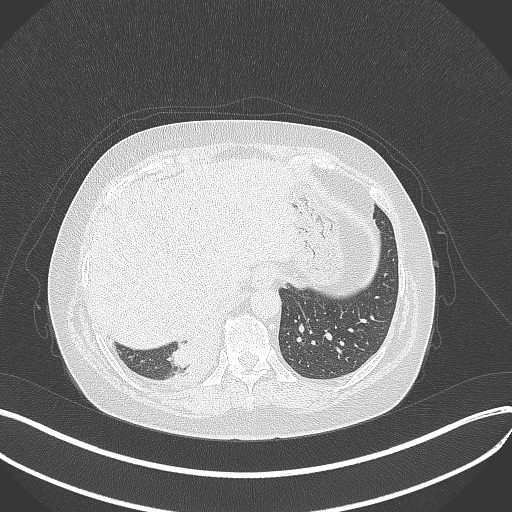
Chest CT, one axial slice; position 78 of 381 along the scan axis; reconstruction kernel B70f; 120 kVp; lung window (W 1500 / L -600 HU); 1 mm slice thickness; 512 × 512 image matrix, field of view 400 × 400 mm. Patient: female, 56 years. From the clinical record (not read from this slice): clinical TNM (as recorded): T2b N1 M0; histopathological grade: G3.
Annotated regions visible in this slice (bounding box drawn by a radiologist):
- lung tumour (recorded histology: small cell carcinoma): bounding box [x1, y1, x2, y2] px = [168, 323, 230, 371]